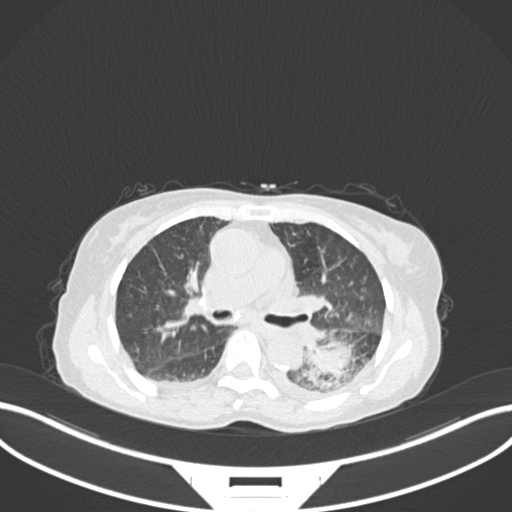
Chest CT, one axial slice; position 104 of 233 along the scan axis; reconstruction kernel B30f; 120 kVp; lung window (W 1500 / L -600 HU); 512 × 512 image matrix, field of view 400 × 400 mm. Female patient, age 78 years. Case-level facts recorded for this patient, not image findings: clinical TNM (as recorded): T3 N0 M1.
Annotated regions visible in this slice (rectangle marked by the reading radiologist):
- lung tumour (recorded histology: squamous cell carcinoma): box from (x=298, y=333) to (x=369, y=394) px